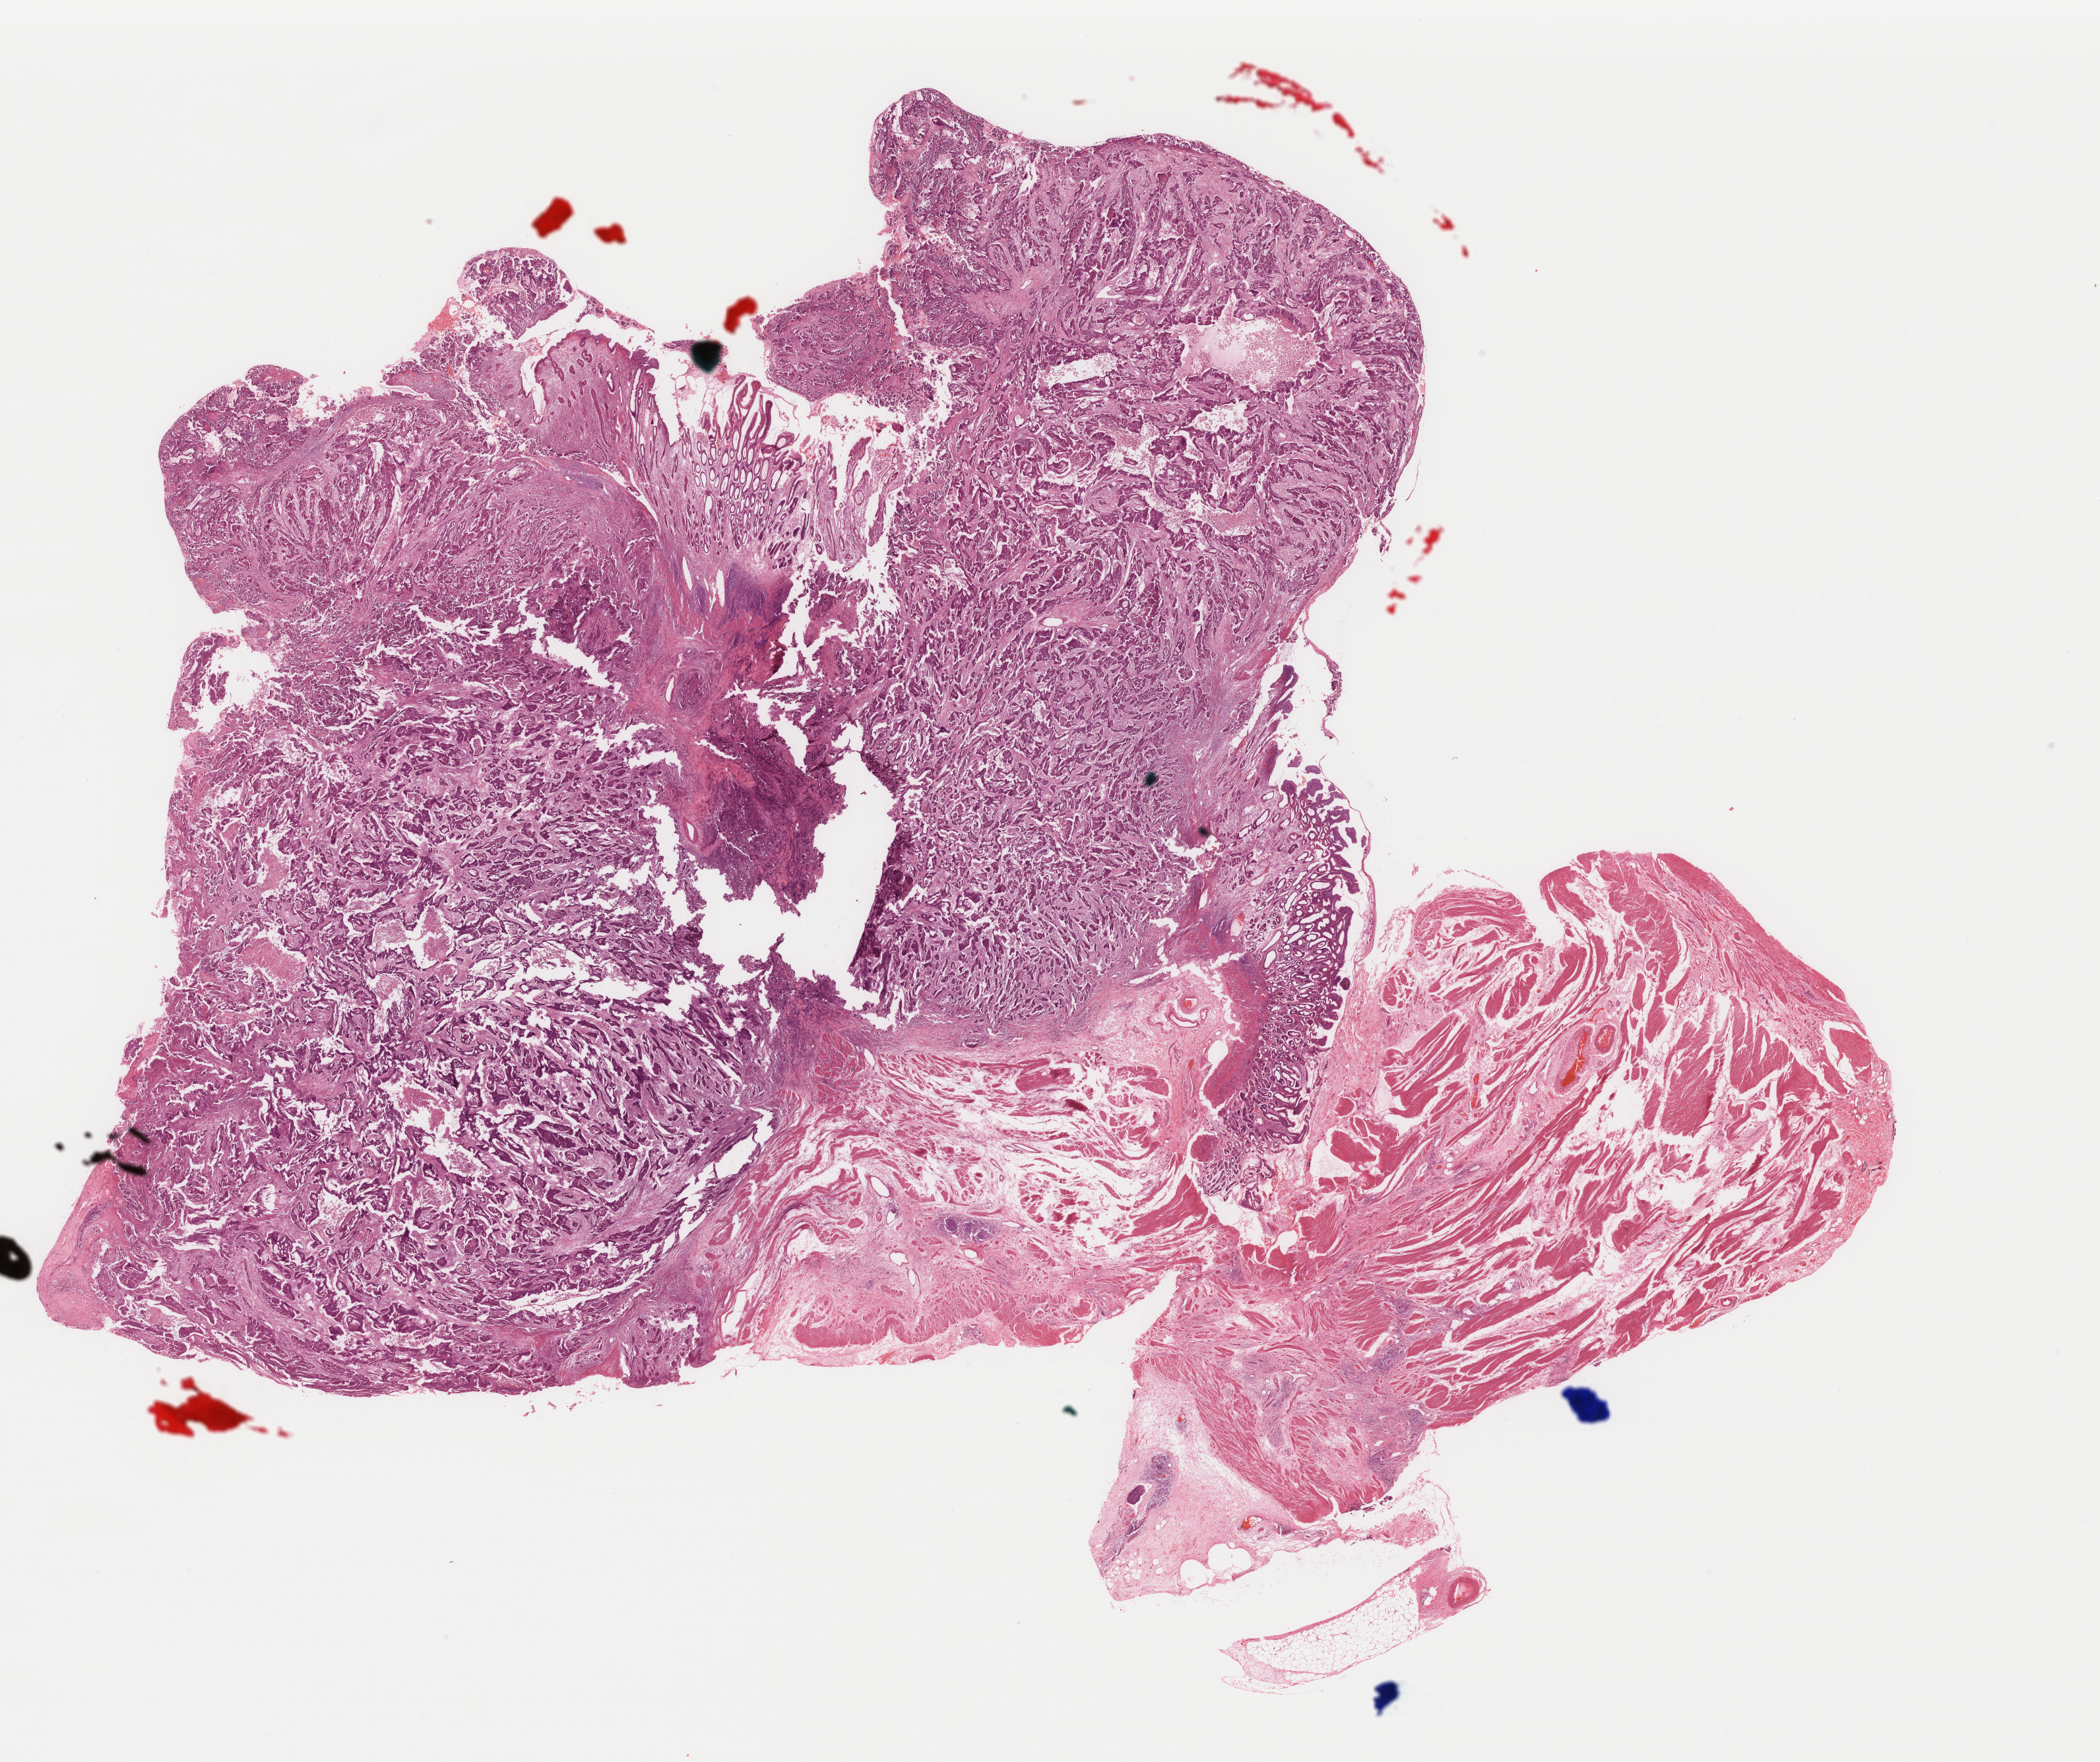
H&E whole-slide image — whole scanned area (about 25.3 x 21.2 mm, slide scanned at 40x) shown as a low-resolution overview, formalin-fixed paraffin-embedded (FFPE) diagnostic section, sample: primary tumour, stomach. Female patient; age at initial diagnosis 68 years. Histologic grade: G2 (moderately differentiated).
- lymph nodes positive (case pathology): 0 of 14 examined
- AJCC pathologic stage: IB (7th edition)
- diagnosis: Adenocarcinoma, NOS (cardia, NOS)